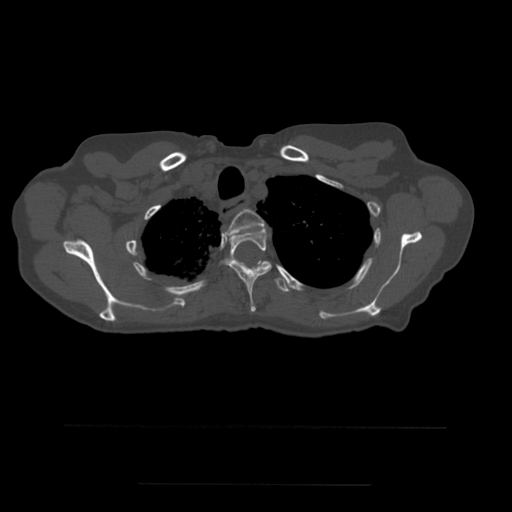
CT including the spine, one axial slice. Bone window (W 1800 / L 400 HU). 1.25 mm slice thickness. 512 × 512 image matrix. Patient age 58 years. Case-level facts recorded for this patient, not image findings: primary cancer: lung.
Structures marked on this image (semi-automatic segmentation, software-assisted and operator-edited):
- T2 vertebra: bounding box [x1, y1, x2, y2] px = [224, 209, 265, 240]
- T3 vertebra: [224, 229, 272, 312]
- T4 vertebra: [242, 263, 290, 292]